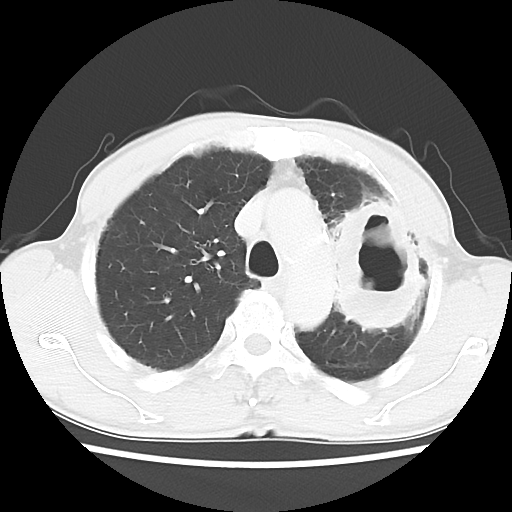
Chest CT, one axial slice. Slice 44 of 60 in the series (ordered by position). Reconstruction kernel LUNG. Lung window (W 1500 / L -600 HU). 5 mm slice thickness. 512 × 512 image matrix, field of view 308 × 308 mm. Male patient, age 64 years. From the clinical record (not read from this slice): clinical TNM (as recorded): T3 N3 M0; histopathological grade: G3.
Outlined on this slice (bounding box drawn by a radiologist):
- lung tumour (recorded histology: adenocarcinoma): bounding box [x1, y1, x2, y2] px = [317, 187, 434, 353]